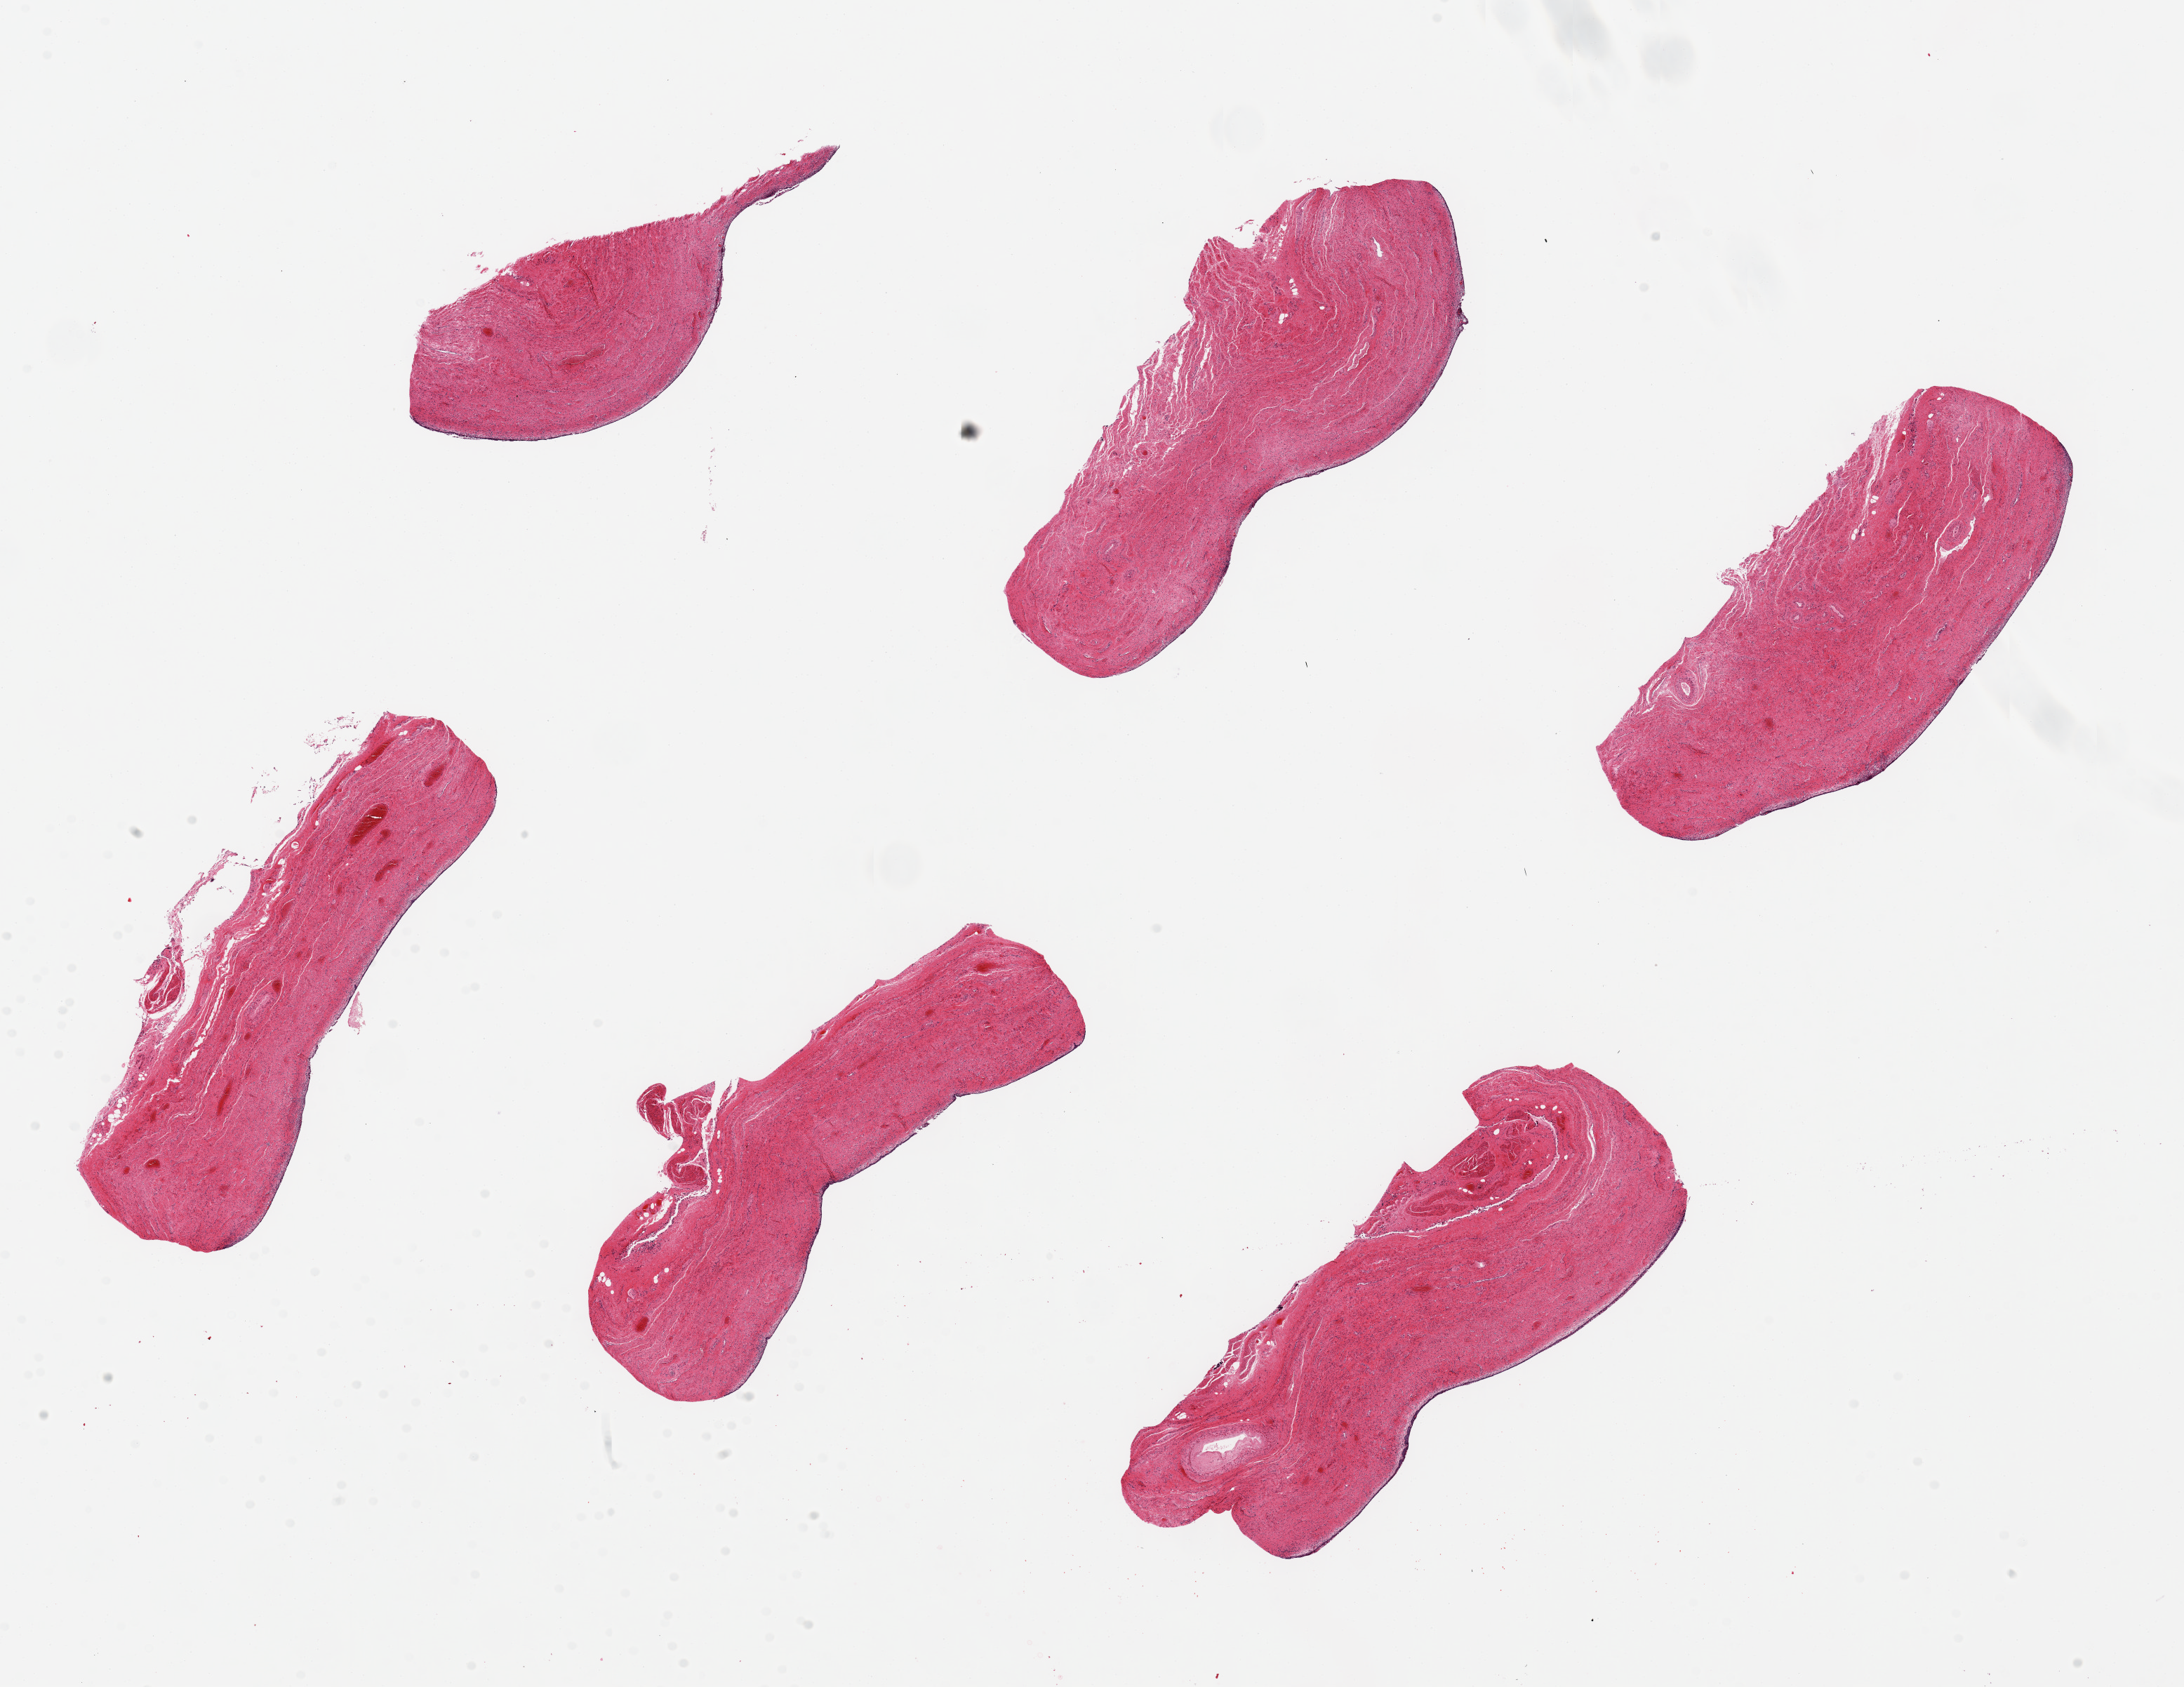
H&E whole-slide image — a low-resolution overview of the entire scanned area, about 24.6 x 19.0 mm; PAXgene-fixed, paraffin-embedded tissue; section of vagina (target tissue); tissue donor sample. Donor sex: female.
Review note (as recorded): 6 pieces ~7x2mm; Essentially all storma, trace sloughing epithelial remnants present.